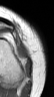
MRI of an extremity soft-tissue mass, one axial slice. Position 15 of 42 along the scan axis. MR volume resampled by the dataset authors to the PET/CT grid (not the native acquisition matrix). 3.27 mm slice thickness. 54 × 97 image matrix, field of view 53 × 95 mm. Female patient. Case-level facts recorded for this patient, not image findings: histological type: spindle cell suggestive of biphasic synovial sarcoma; grade: intermediate; site of the primary tumour: left knee.
Annotated regions visible in this slice (expert contour drawn on MRI and transferred to this co-registered scan by the dataset authors):
- gross tumour volume including surrounding oedema: bounding box <17,46,31,75> (left, top, right, bottom; pixels)
- gross tumour volume (mass): <17,46,31,74>